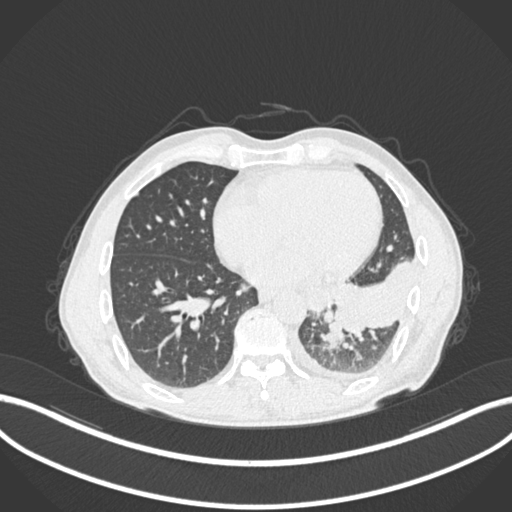
Chest CT, one axial slice; position 86 of 222 along the scan axis; reconstruction kernel B30f; lung window (W 1500 / L -600 HU); 512 × 512 image matrix, field of view 400 × 400 mm. Male patient, age 47 years. Case-level facts recorded for this patient, not image findings: clinical TNM (as recorded): T3 N1 M1c.
Structures marked on this image (rectangle marked by the reading radiologist):
- lung tumour (recorded histology: small cell carcinoma): bounding box (x1, y1, x2, y2) in pixels: (318, 321, 347, 352)